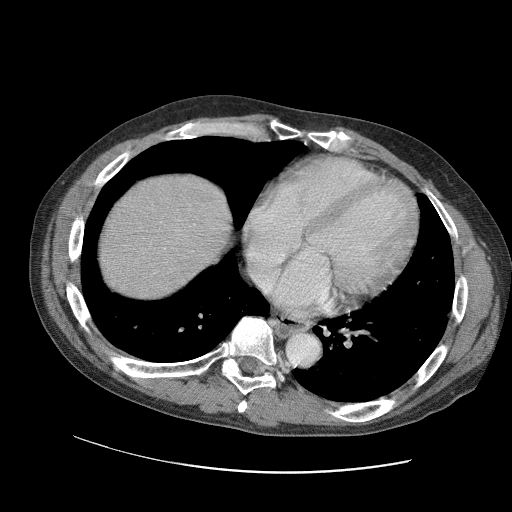
Contrast-enhanced abdominal CT (liver protocol), one axial slice. Slice 94 of 109 in the series (ordered by position). 120 kVp. Soft-tissue window (W 400 / L 40 HU). 512 × 512 image matrix, field of view 400 × 400 mm. From the clinical record (not read from this slice): diagnosis: hepatocellular carcinoma (patient treated with transarterial chemoembolisation; whether this scan precedes or follows treatment is not stated here); TNM stage (as recorded): Stage-IIIC; Child-Pugh class: B; tumour differentiation: well differentiated; tumour nodularity: uninodular.
Annotated regions visible in this slice (semi-automatic segmentation, software-assisted and operator-edited):
- liver parenchyma outside the tumour (the mass and vessels are separate outlines, so this box may not span the whole liver): box from (x=96, y=174) to (x=230, y=300) px
- liver vessels: (x=178, y=224)–(x=194, y=253)